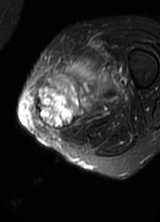
MRI of an extremity soft-tissue mass, one axial slice. T2-weighted fat-saturated. MR volume resampled by the dataset authors to the PET/CT grid (not the native acquisition matrix). 3.27 mm slice thickness. 160 × 222 image matrix. Female patient. Case-level facts recorded for this patient, not image findings: histological type: pleomorphic leiomyosarcoma; grade: high; site of the primary tumour: left thigh.
Outlined on this slice (expert contour drawn on MRI and transferred to this co-registered scan by the dataset authors):
- gross tumour volume including surrounding oedema: bounding box (x1, y1, x2, y2) in pixels: (36, 56, 122, 131)
- gross tumour volume (mass): (36, 81, 92, 130)